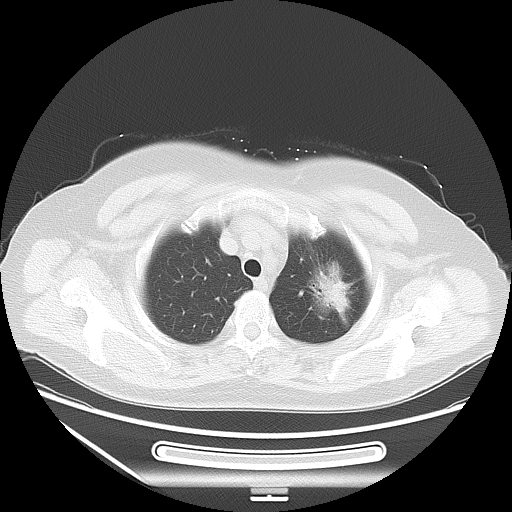
Chest CT, one axial slice. Slice 46 of 53 in the series (ordered by position). Reconstruction kernel LUNG. Lung window (W 1500 / L -600 HU). 5 mm slice thickness. 512 × 512 image matrix, field of view 403 × 403 mm. Female patient, age 66 years. From the clinical record (not read from this slice): clinical TNM (as recorded): T2 N0 M0.
Annotated regions visible in this slice (rectangle marked by the reading radiologist):
- lung tumour (recorded histology: adenocarcinoma): bounding box (x1, y1, x2, y2) in pixels: (302, 256, 357, 328)